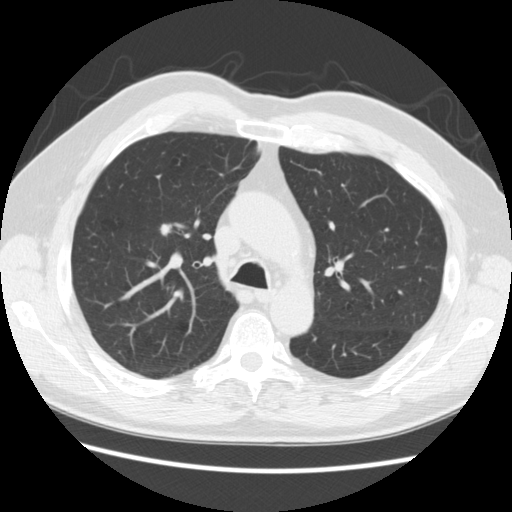
Low-dose screening chest CT, axial slice; baseline screening round; lung window (W 1500 / L -600 HU); 2.5 mm slice thickness; standard (soft-tissue) reconstruction kernel (STANDARD); slice 84 of 259 in the series. Male, age 69 years at enrolment. Former smoker at enrolment.
Expert reader's lesion annotation, box from (x=150, y=217) to (x=192, y=249) px. Reader record for this screening exam (exam-level; its link to the box is not recorded): non-calcified nodule or mass ≥4 mm, right upper lobe, 9 × 7 mm, poorly defined margins, soft tissue attenuation. Lung cancer was diagnosed 50 days after this screen: adenocarcinoma, NOS, right upper lobe, moderately differentiated (G2), stage IA (AJCC 6th edition), 9 mm at pathology.